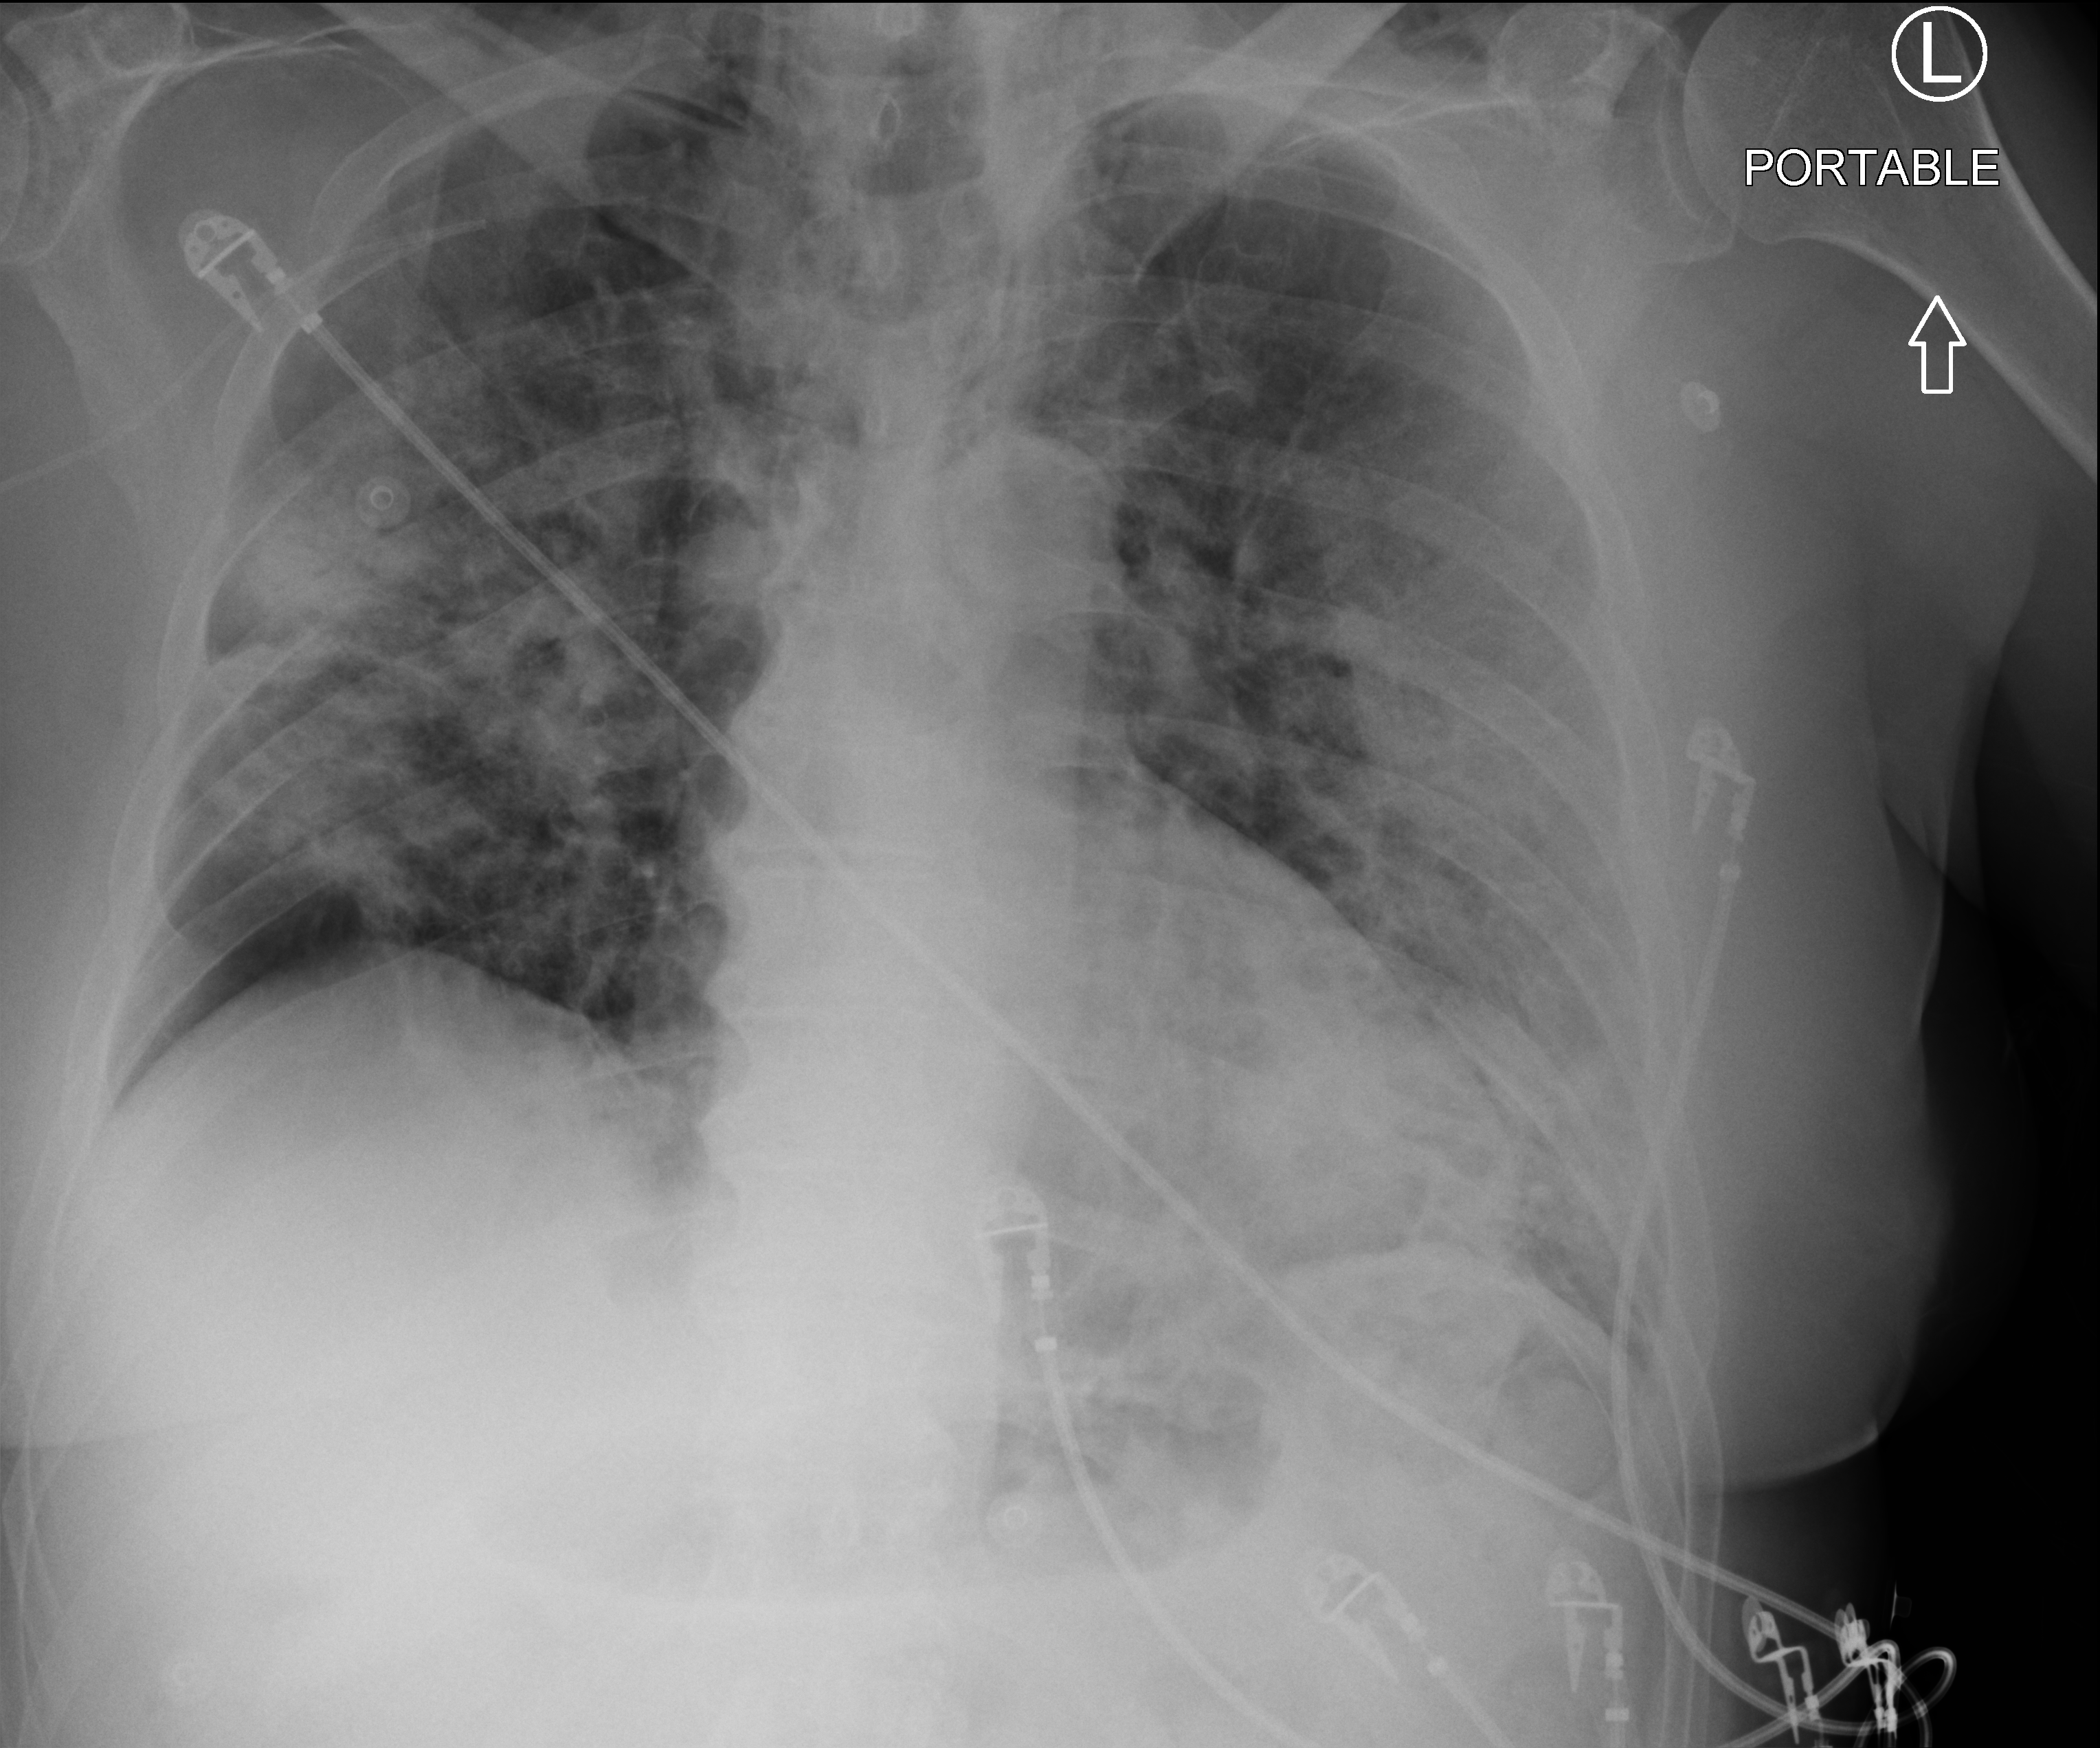
Portable chest radiograph; anteroposterior (AP) projection. Patient hospitalised with COVID-19; male, aged 60–74 years.
Hospital-stay facts (about this admission, not read from this image; timing relative to this image not recorded):
- admitted to intensive care during this hospital stay: no
- other chronic lung disease (admission record): no